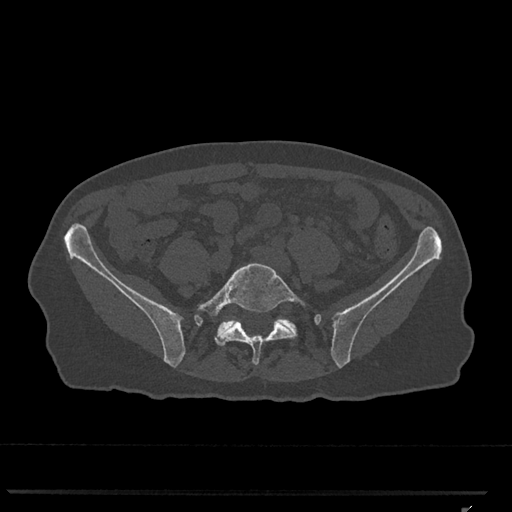
CT including the spine, one axial slice; slice 142 of 793 in the series (ordered by position); reconstruction kernel Br40s/3; 120 kVp; bone window (W 1800 / L 400 HU); 512 × 512 image matrix, field of view 380 × 380 mm. Female patient, age 62 years. Case-level facts recorded for this patient, not image findings: primary cancer: renal.
Outlined on this slice (semi-automatically segmented with operator editing):
- L5 vertebra: bounding box <197,263,307,365> (left, top, right, bottom; pixels)